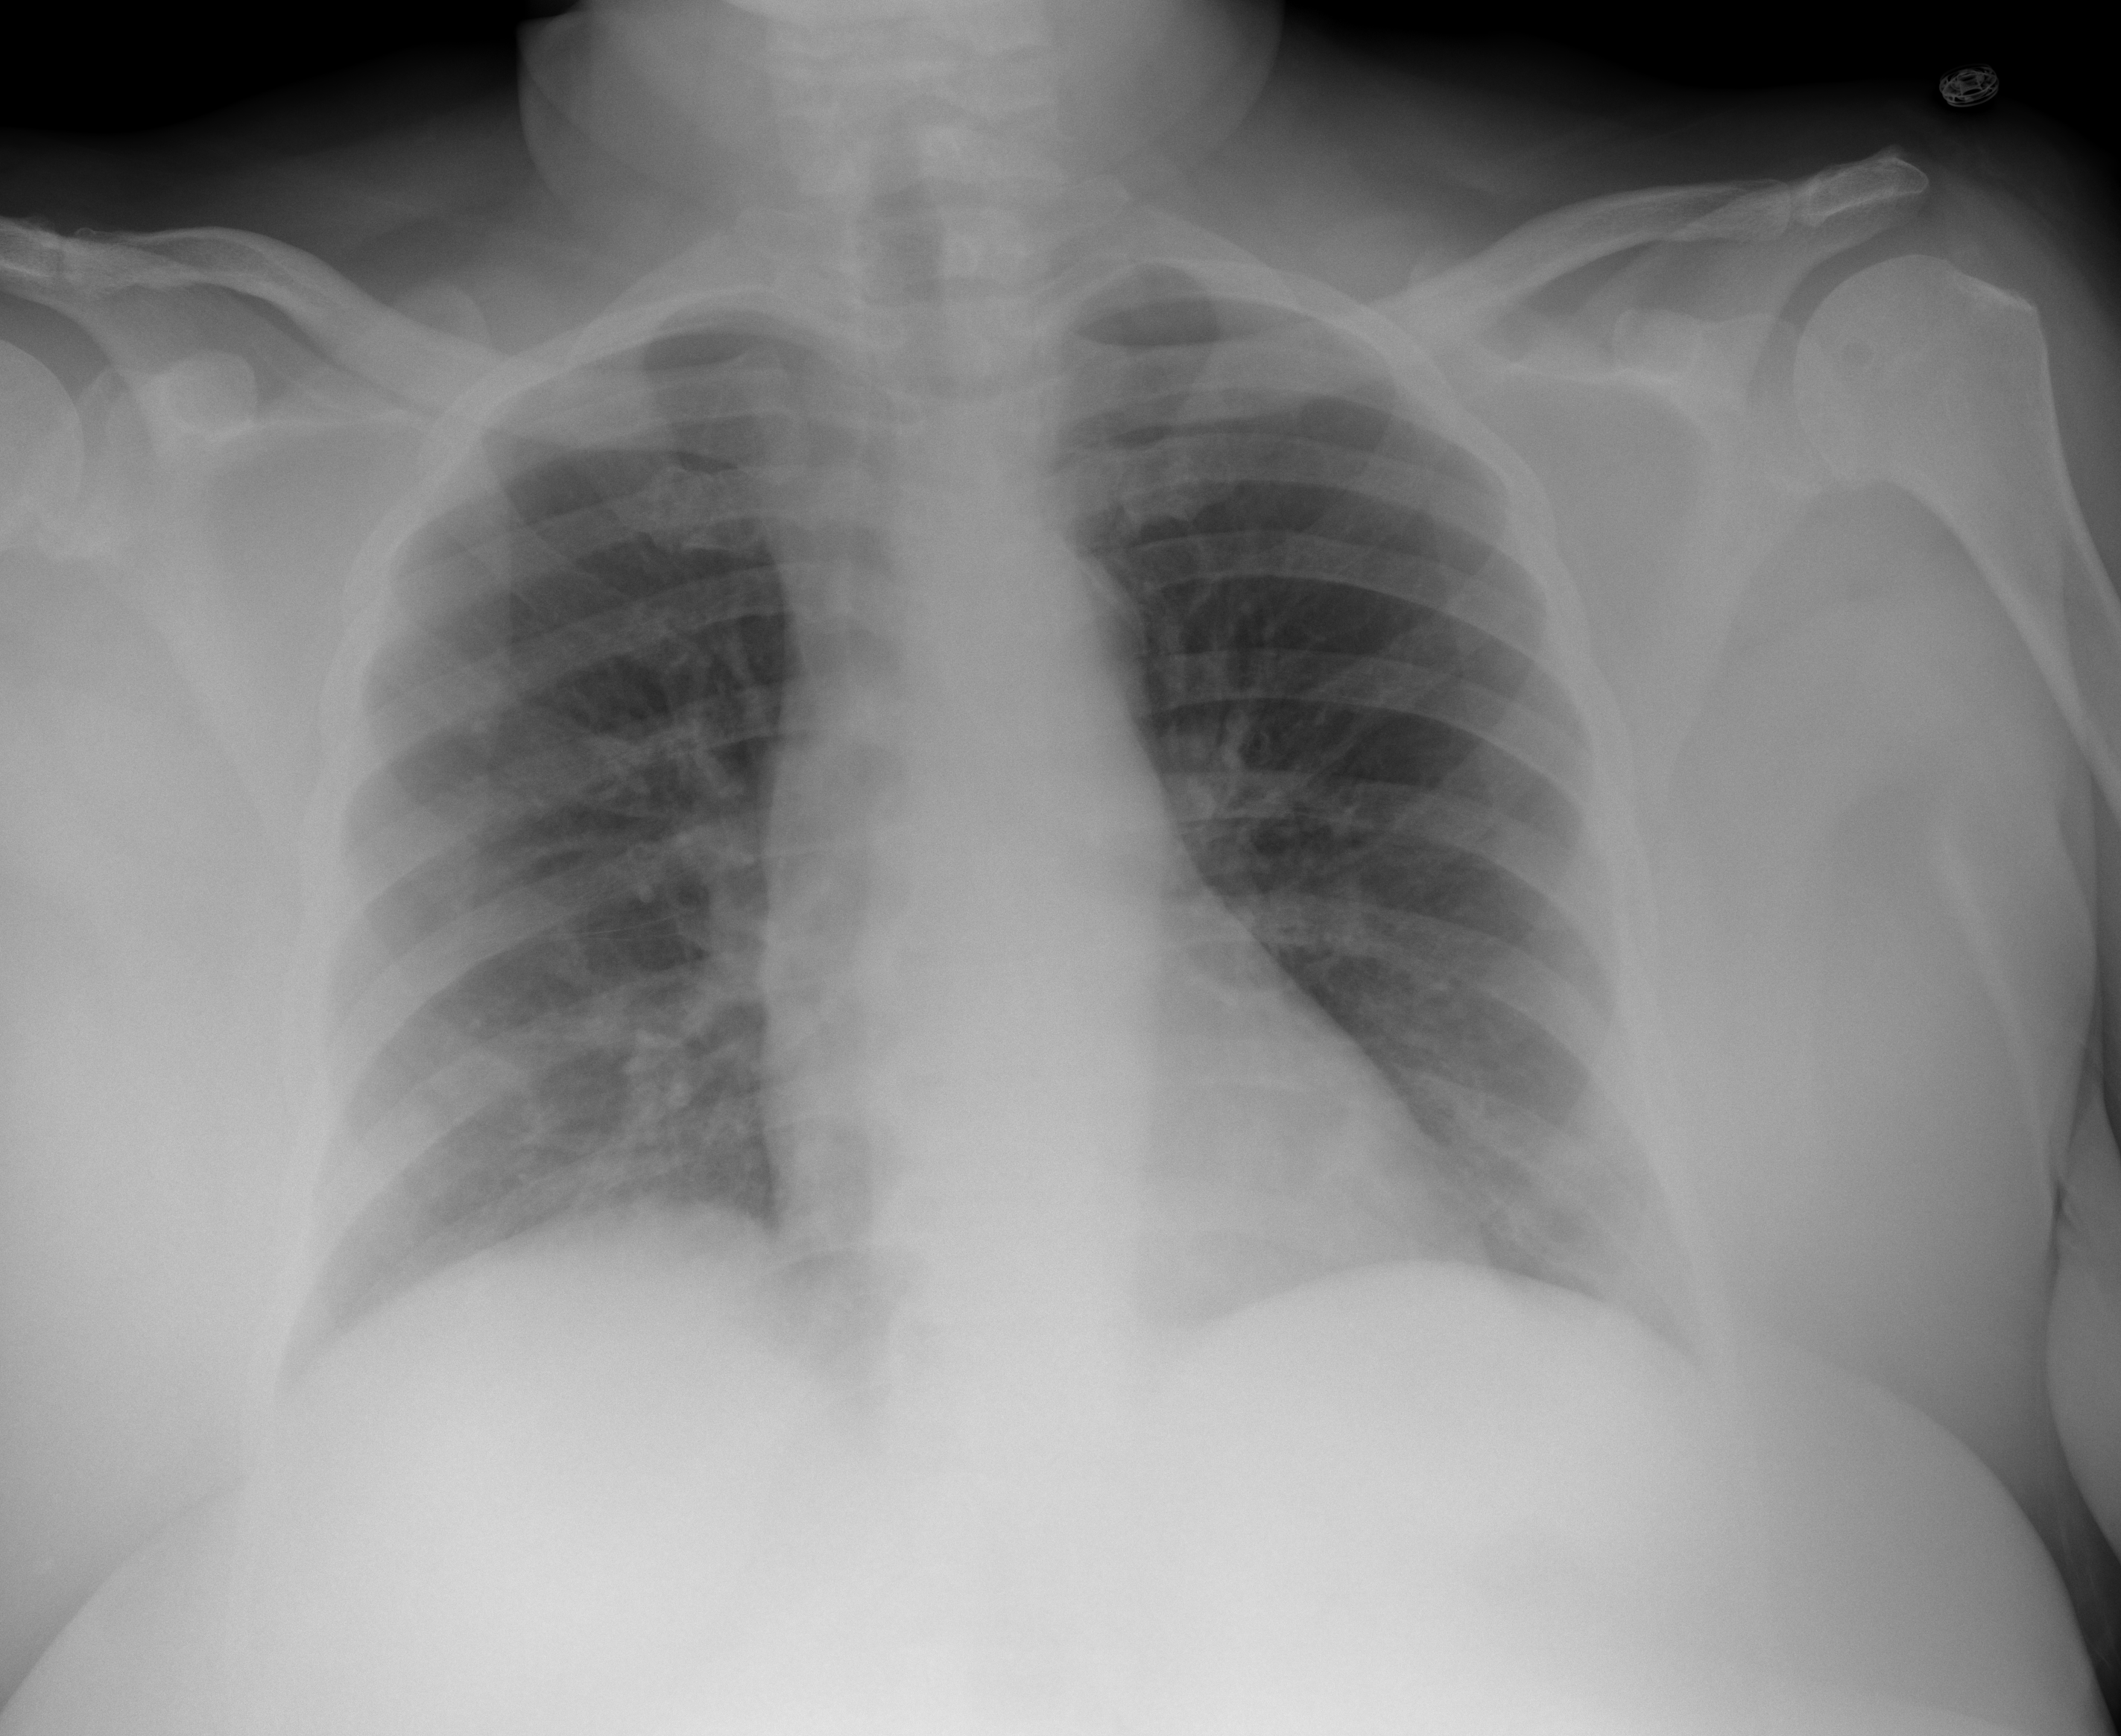
Chest X-ray (portable), AP projection. Female patient, age 61 years; imaged 7 days after the COVID-19 diagnosis.
Radiologist key findings (as recorded): ill-defined densities at the lung bases left greater than the right.